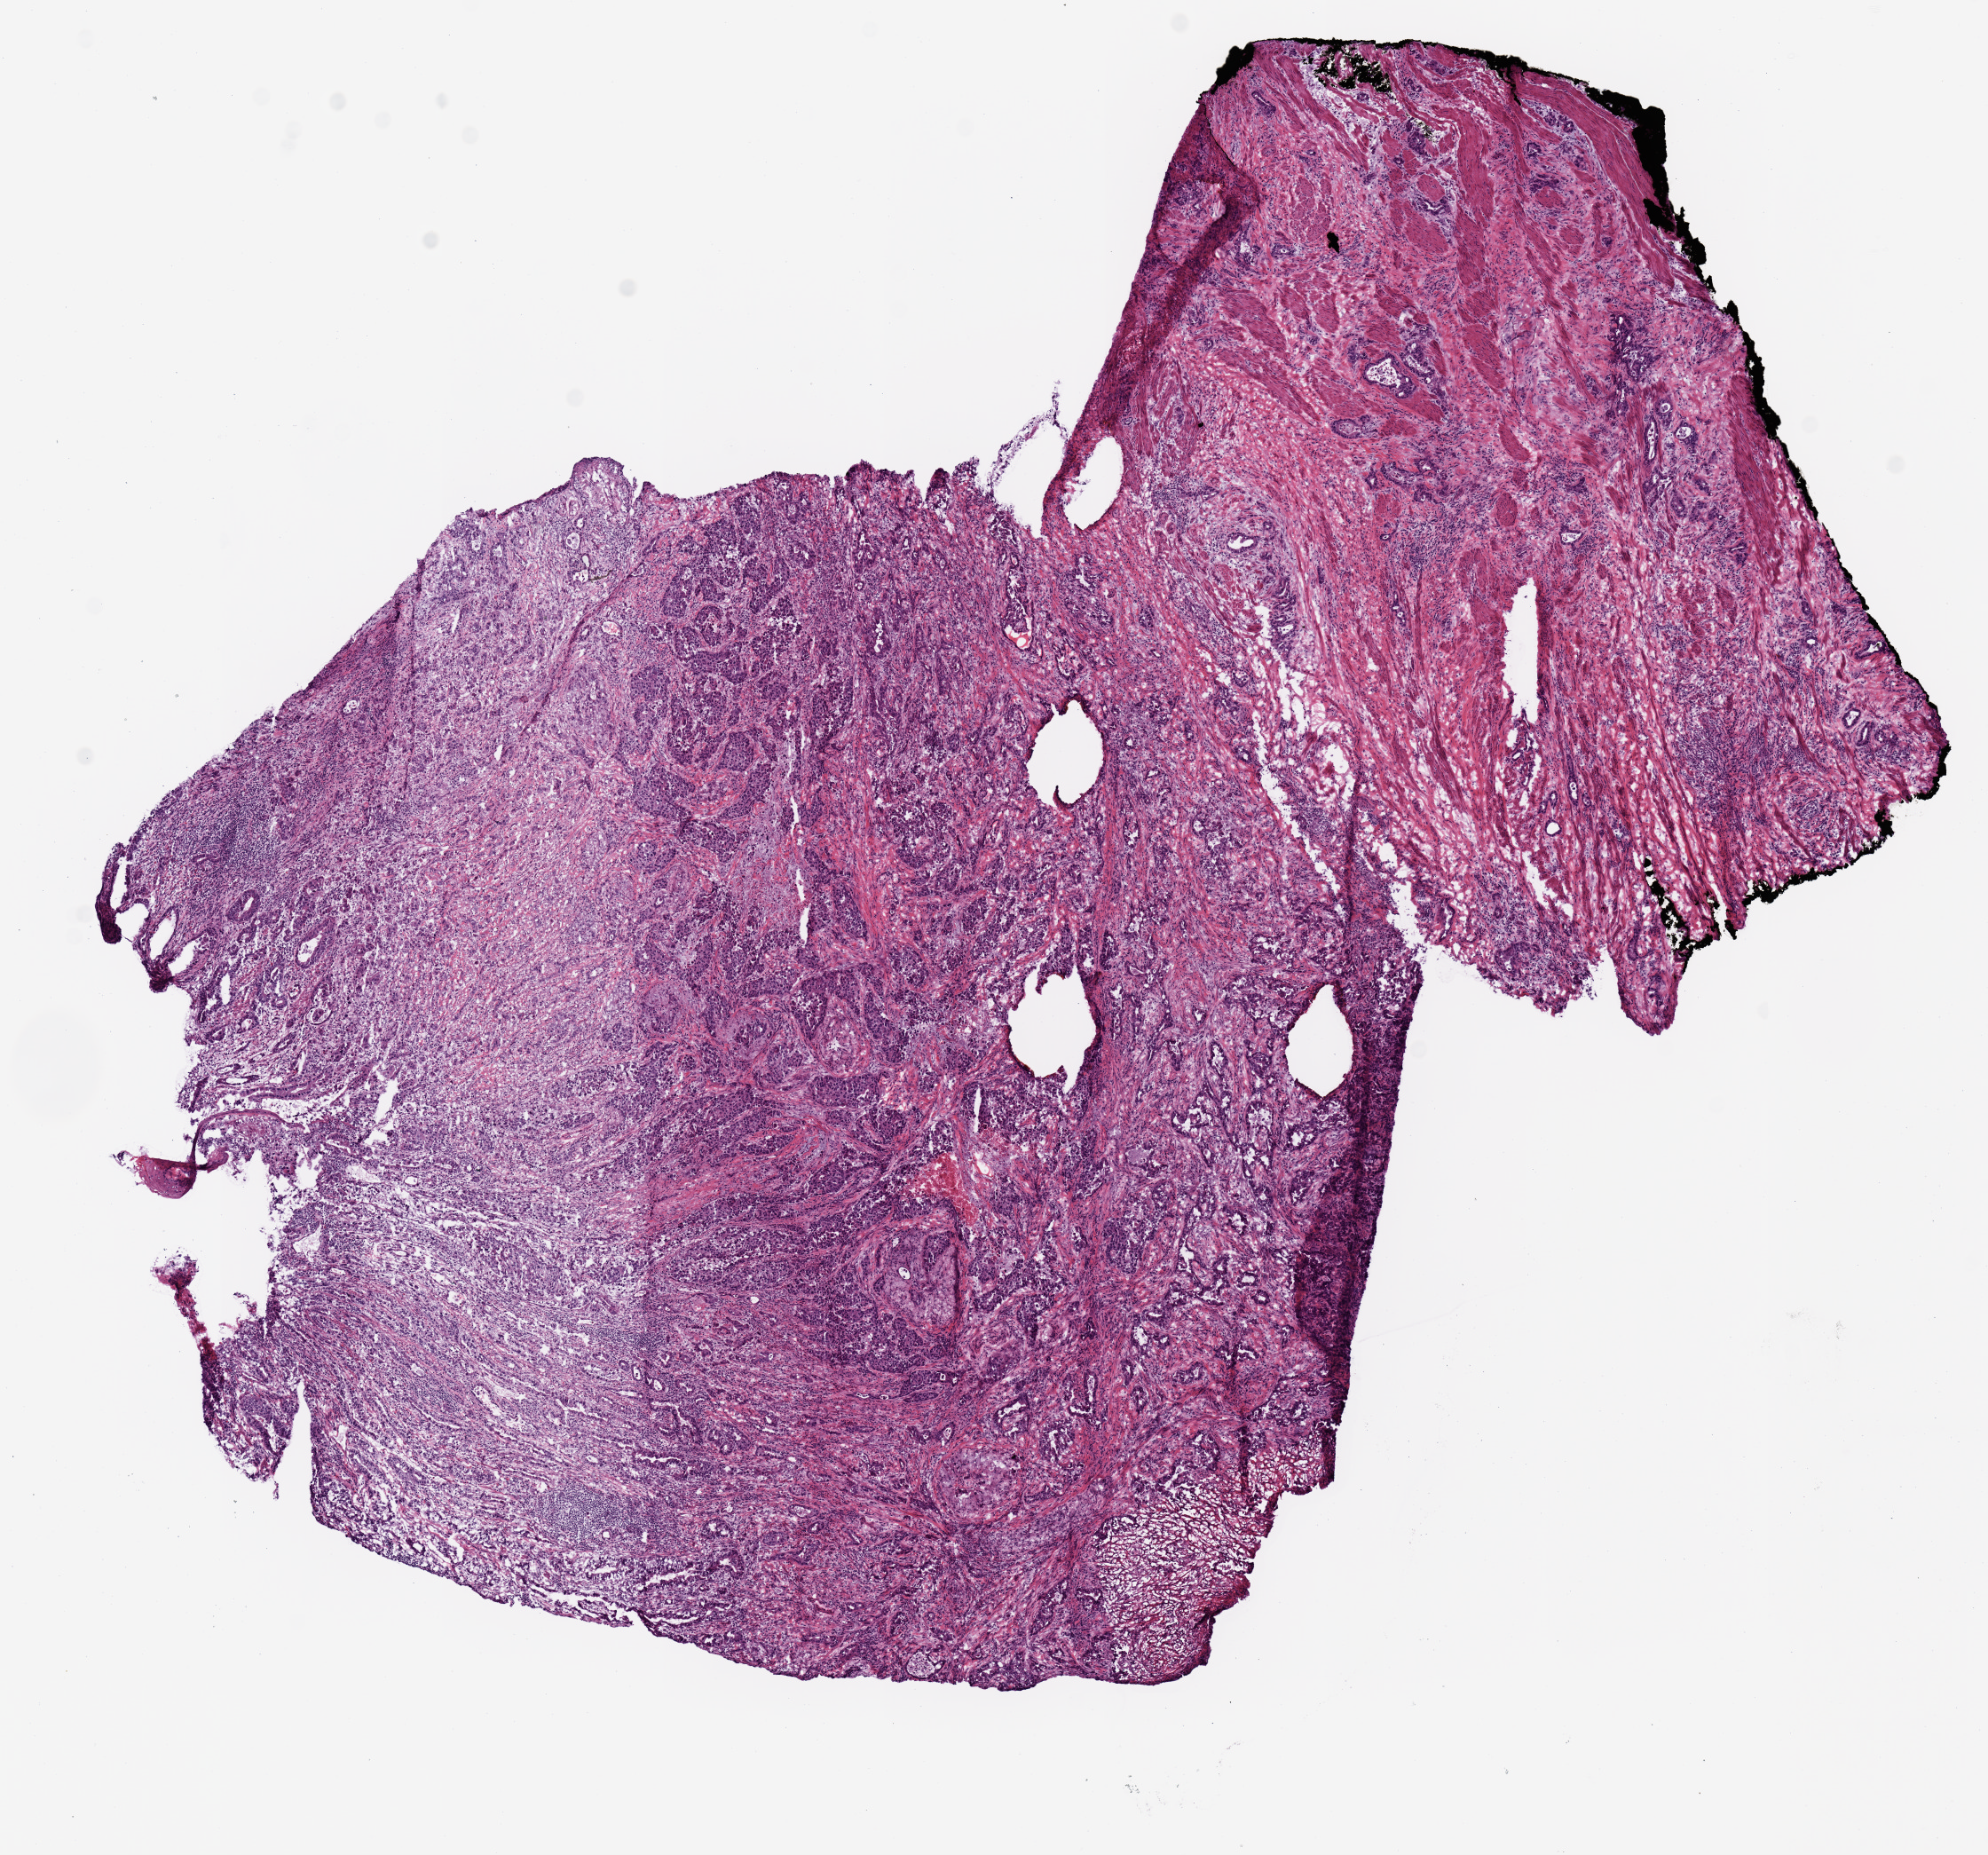
Digitized H&E tissue section (whole slide), shown as a low-resolution overview of the whole scanned area (about 8.9 x 8.3 mm); frozen section from the top of the tissue portion; sample: primary tumour, stomach. Male, age 79 years at initial diagnosis. Histologic grade: G2 (moderately differentiated). Pathologist review of this section (percent, as recorded): tumour cells 98%, tumour nuclei 65%, normal cells 0%, stromal cells 0%, necrosis 2%. Infiltration values recorded for this section: lymphocyte infiltration 15%, monocyte infiltration 0%, neutrophil infiltration 10%.
• lymph nodes positive (case pathology): 0 of 13 examined
• AJCC pathologic stage: IIA
• histologic diagnosis: Adenocarcinoma, NOS (cardia, NOS)